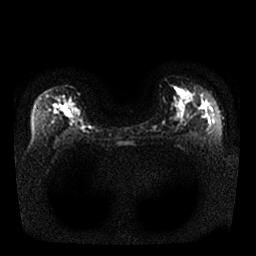
Breast MRI, one axial slice; slice 17 of 25 in the series (ordered by position); diffusion-weighted series; image 2 of 4 stored at this slice position (different b-values; order by instance number); 1.5 T; 4 mm slice thickness; 256 × 256 image matrix, field of view 340 × 340 mm. Female patient.
Structures marked on this image (expert manual segmentation):
- tumour on diffusion-weighted imaging: bounding box (x1, y1, x2, y2) in pixels: (61, 107, 76, 119)